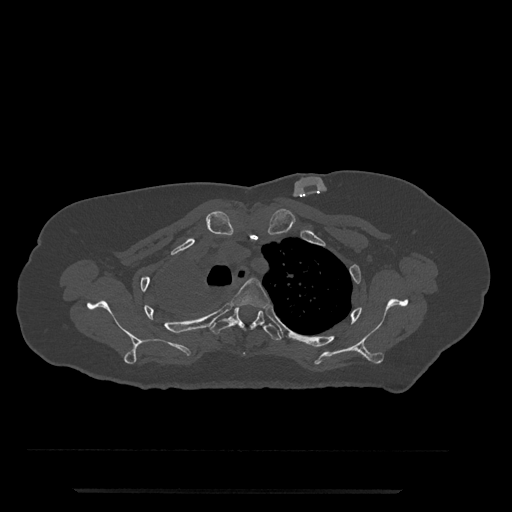
CT including the spine, one axial slice. Slice 609 of 797 in the series (ordered by position). Reconstruction kernel Br40s/3. Bone window (W 1800 / L 400 HU). 0.5 mm slice thickness. 512 × 512 image matrix, field of view 440 × 440 mm. Female patient, age 51 years. From the clinical record (not read from this slice): primary cancer: neuro.
Structures marked on this image (semi-automatic segmentation, software-assisted and operator-edited):
- T3 vertebra: bounding box [x1, y1, x2, y2] px = [233, 278, 270, 309]
- T4 vertebra: [209, 307, 282, 341]